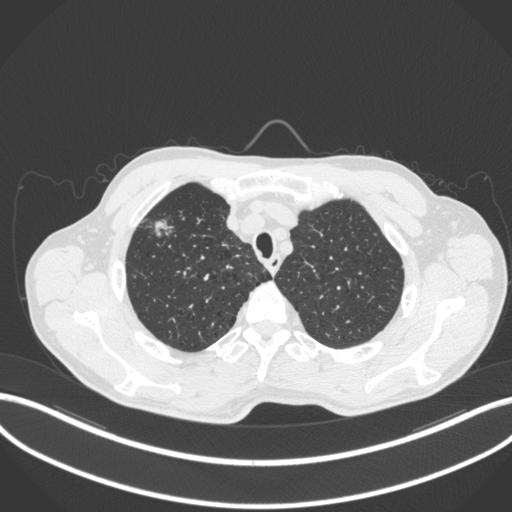
Chest CT, one axial slice; slice 354 of 414 in the series (ordered by position); reconstruction kernel B31f; 120 kVp; lung window (W 1500 / L -600 HU); 1 mm slice thickness; 512 × 512 image matrix. Male patient, age 69 years. Case-level facts recorded for this patient, not image findings: clinical TNM (as recorded): T1b N1 M0.
Structures marked on this image (bounding box drawn by a radiologist):
- lung tumour (recorded histology: adenocarcinoma): box from (x=155, y=210) to (x=171, y=239) px